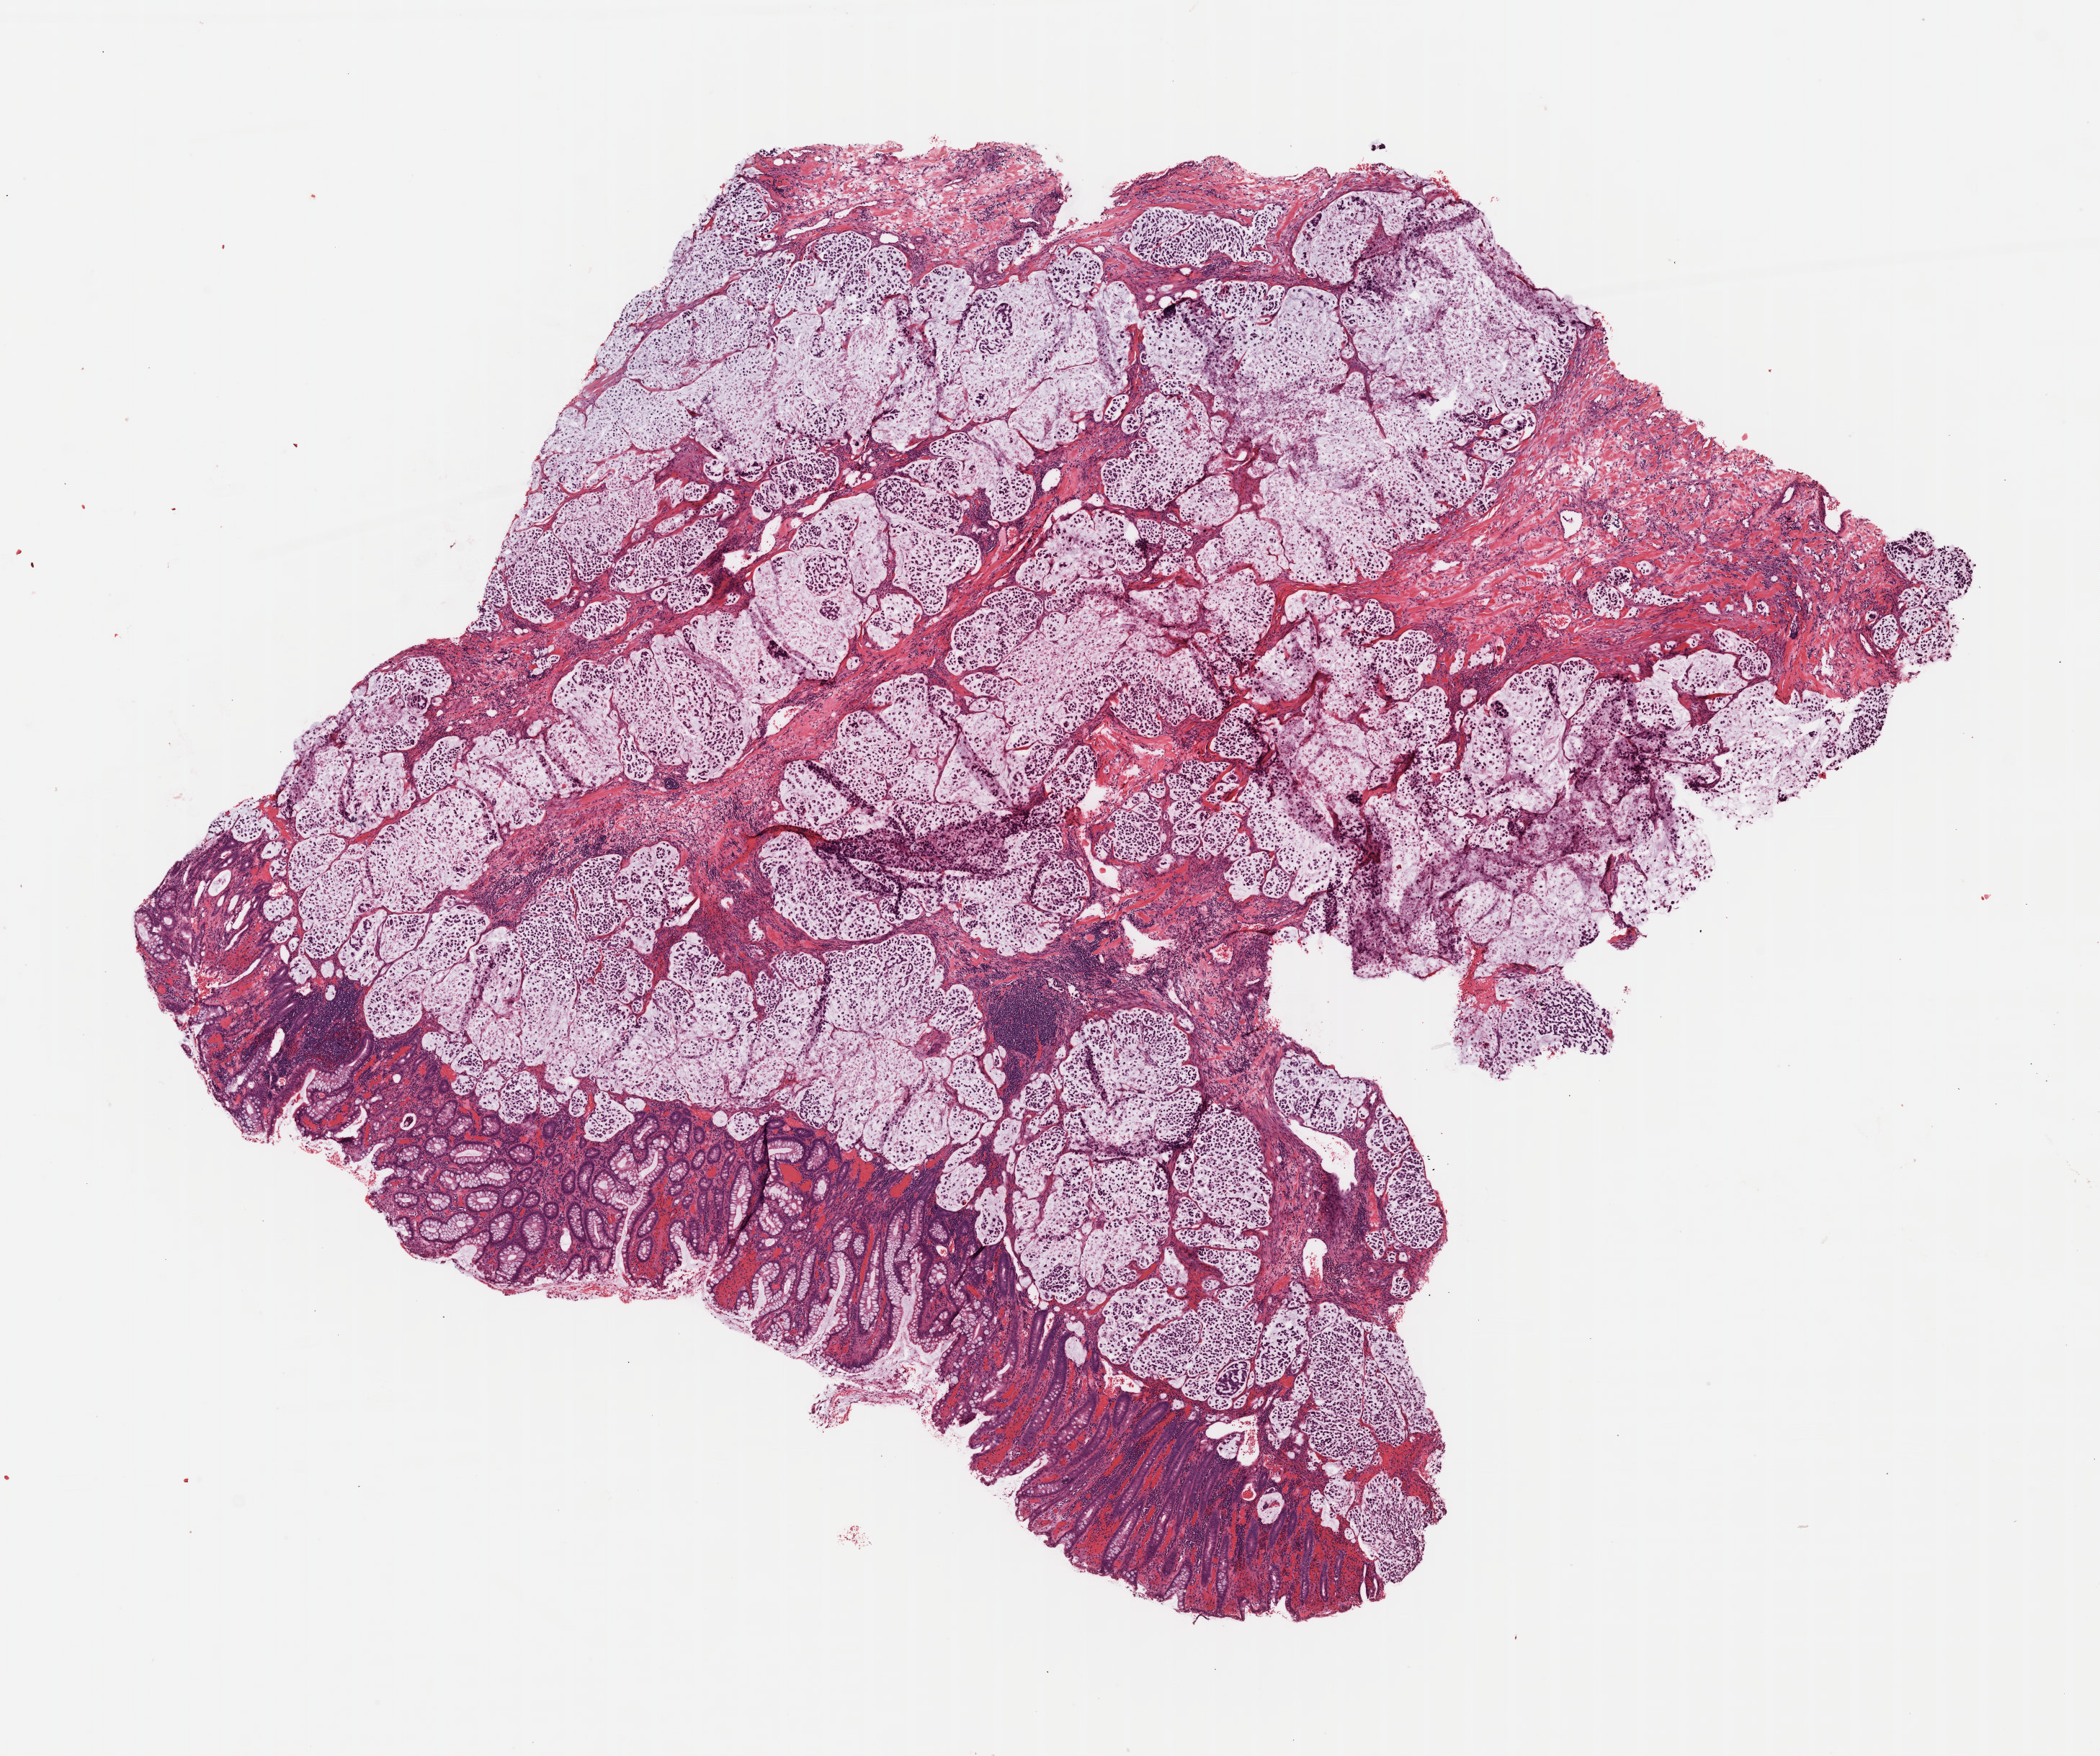
Hematoxylin and eosin (H&E) stained whole-slide image — low-resolution overview of the scanned area, about 11.5 x 9.6 mm; formalin-fixed paraffin-embedded (FFPE) diagnostic section; primary tumour sample from the colon. Patient: female, age at initial diagnosis 34 years.
• TNM: T3 N2 MX
• pathologic diagnosis: Mucinous adenocarcinoma (transverse colon)
• lymph nodes positive (case pathology): 13 of 41 examined
• AJCC pathologic stage: IIIC